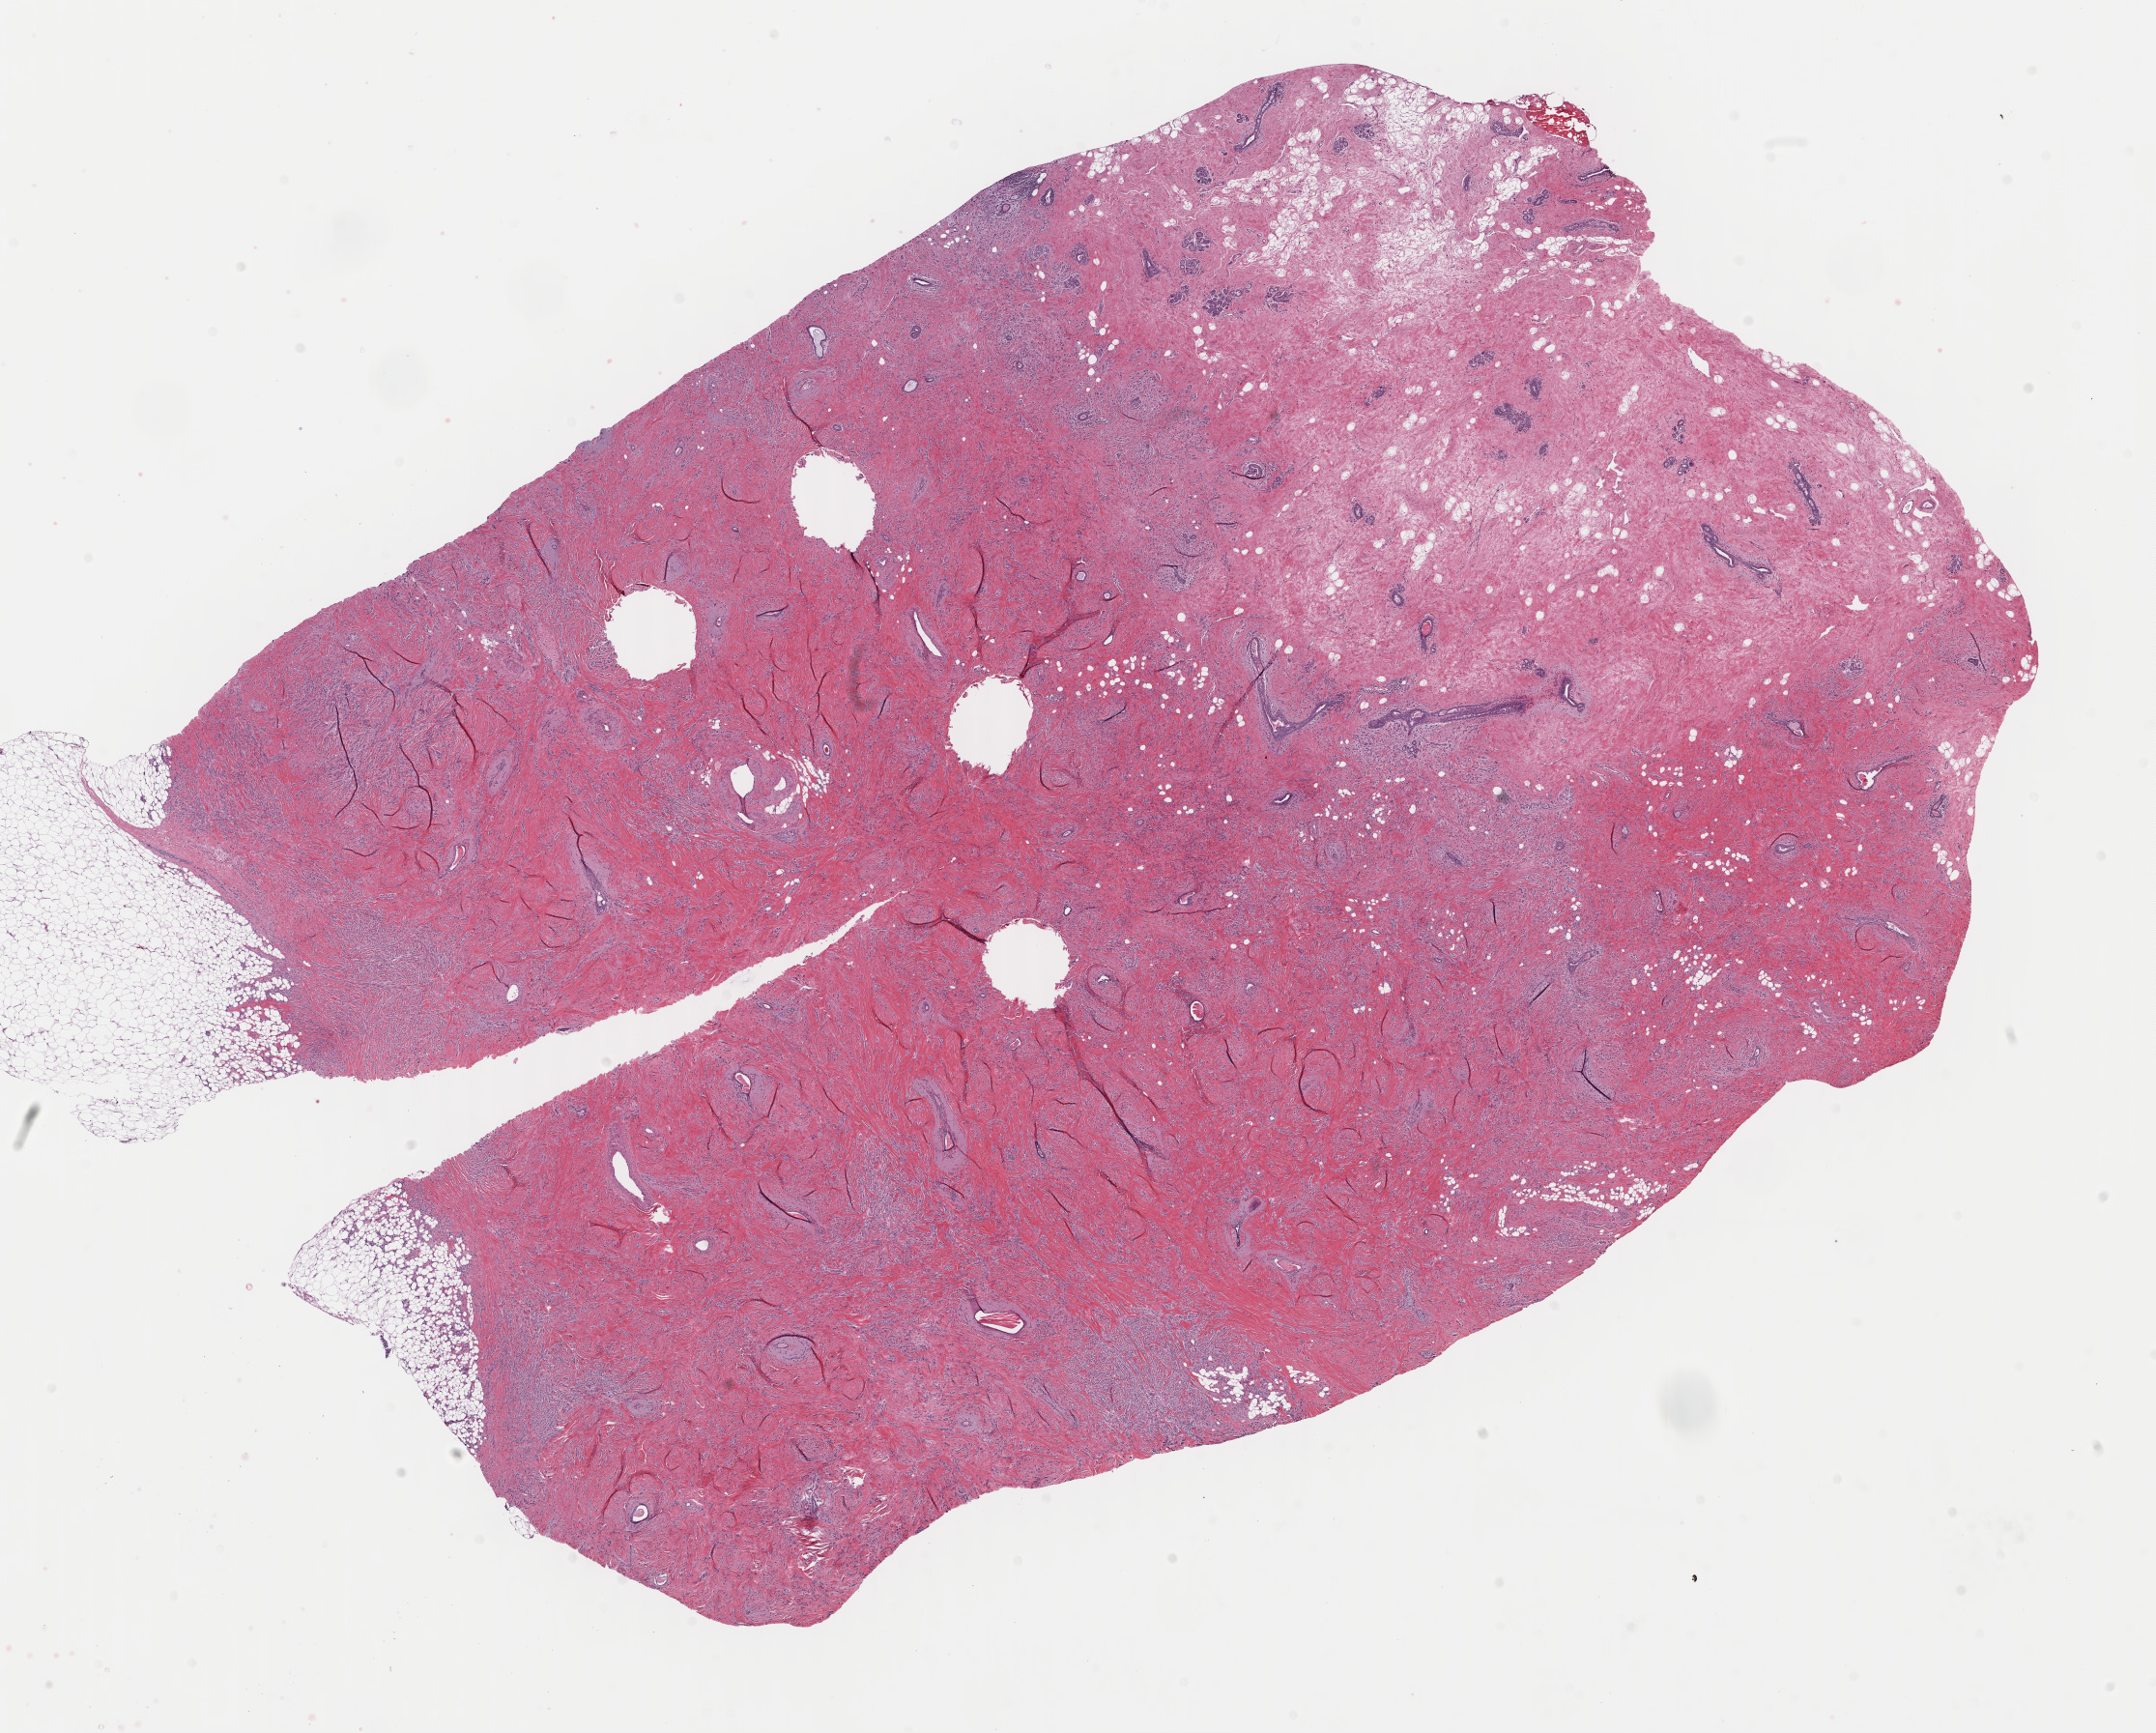
Whole-slide histology image, H&E-stained, low-resolution overview of the scanned area, about 17.6 x 14.2 mm (from a 40x scan). Formalin-fixed paraffin-embedded (FFPE) diagnostic section. Breast, primary tumour sample. Female, age 60 years at initial diagnosis.
* lymph nodes positive (case pathology): 3 of 15 examined
* AJCC pathologic stage: IIIA (6th edition)
* histologic diagnosis: Lobular carcinoma, NOS